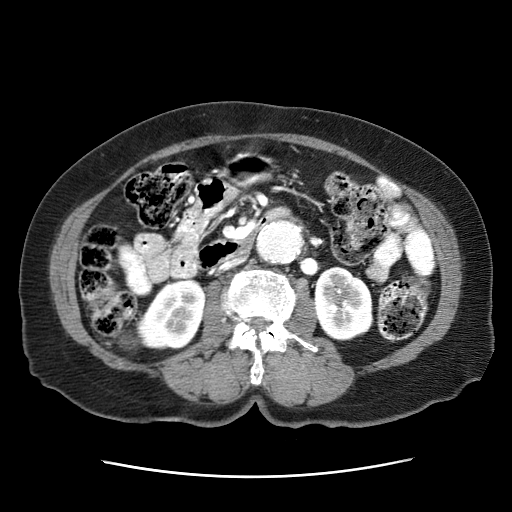
Contrast-enhanced abdominal CT (liver protocol), one axial slice. Position 1 of 63 along the scan axis. Reconstruction kernel STANDARD. 120 kVp. Intravenous contrast given. Soft-tissue window (W 400 / L 40 HU). 2.5 mm slice thickness. 512 × 512 image matrix, field of view 360 × 360 mm. Female patient, age 79 years. Case-level facts recorded for this patient, not image findings: diagnosis: hepatocellular carcinoma (patient treated with transarterial chemoembolisation; whether this scan precedes or follows treatment is not stated here); TNM stage (as recorded): Stage-II; Child-Pugh class: B; tumour differentiation: well differentiated; tumour nodularity: multinodular.
Structures marked on this image (semi-automatic segmentation, software-assisted and operator-edited):
- abdominal aorta: box from (x=256, y=221) to (x=303, y=264) px